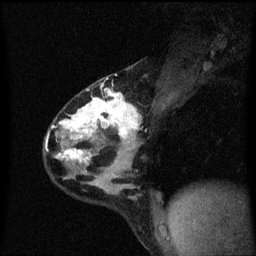
Breast MRI (dynamic contrast-enhanced), one sagittal slice; slice 38 of 60 in the series (ordered by position); dynamic contrast-enhanced series, image 2 of 3 at this slice position (ordered by acquisition); 1.5 T; TE 4.2 ms, TR 8.4 ms; 2 mm slice thickness; 256 × 256 image matrix, field of view 200 × 200 mm. Patient: female, 32 years.
Annotated regions visible in this slice (semi-automatic segmentation, software-assisted and operator-edited):
- analysis volume of interest (the breast-tissue region the enhancement analysis was run in; not a lesion): bounding box (x1, y1, x2, y2) in pixels: (44, 74, 142, 169)
- tumour enhancement mask (voxels above the 70 % enhancement threshold inside the analysis volume of interest): (46, 88, 141, 163)